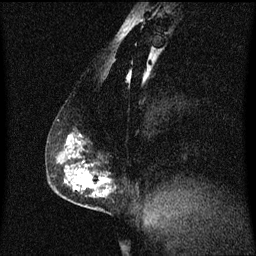
Breast MRI (dynamic contrast-enhanced), one sagittal slice. Slice 28 of 60 in the series (ordered by position). Dynamic contrast-enhanced series, image 2 of 3 at this slice position (ordered by acquisition). 1.5 T. TE 4.2 ms, TR 8.4 ms. 256 × 256 image matrix, field of view 200 × 200 mm. Female patient, age 40 years. Case-level facts recorded for this patient, not image findings: setting: breast cancer imaged before/during neoadjuvant chemotherapy; receptor status: triple-negative.
Outlined on this slice (semi-automatically segmented with operator editing):
- analysis volume of interest (the breast-tissue region the enhancement analysis was run in; not a lesion): bounding box <58,132,113,211> (left, top, right, bottom; pixels)
- tumour enhancement mask (voxels above the 70 % enhancement threshold inside the analysis volume of interest): <66,138,107,197>